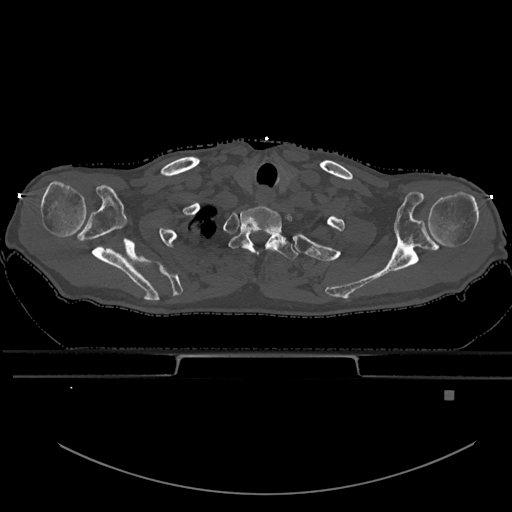
CT including the spine, one axial slice. Position 547 of 969 along the scan axis. Bone window (W 1800 / L 400 HU). 512 × 512 image matrix. Male patient, age 82 years. Case-level facts recorded for this patient, not image findings: primary cancer: prostate; vertebrae with lytic lesions (as recorded): T11, T9, T8, T2.
Outlined on this slice (semi-automatic segmentation, software-assisted and operator-edited):
- T1 vertebra: box from (x=229, y=227) to (x=298, y=260) px